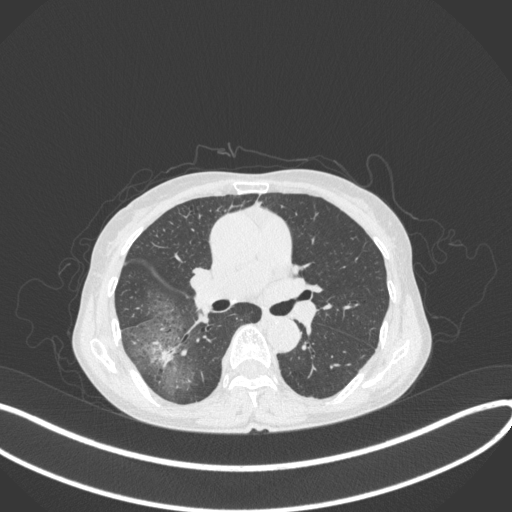
Chest CT, one axial slice; position 228 of 379 along the scan axis; reconstruction kernel B31f; 120 kVp; lung window (W 1500 / L -600 HU); 1 mm slice thickness; 512 × 512 image matrix, field of view 400 × 400 mm. Patient: female, 69 years. From the clinical record (not read from this slice): clinical TNM (as recorded): T1b N0 M0.
Outlined on this slice (rectangle marked by the reading radiologist):
- lung tumour (recorded histology: adenocarcinoma): bounding box [x1, y1, x2, y2] px = [145, 336, 177, 370]